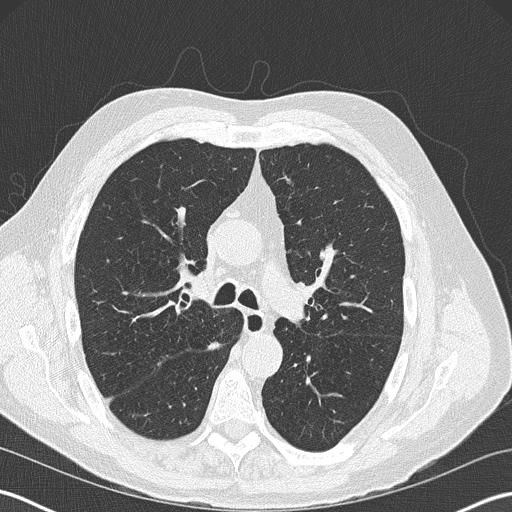
Low-dose screening chest CT, one axial slice. Position 123 of 199 along the scan axis. Reconstruction kernel B50f. Lung window (W 1500 / L -600 HU). 512 × 512 image matrix.
Annotated regions visible in this slice (outlined manually by an expert reader):
- lesion 1 (tumor, upper lobe of right lung): box from (x=153, y=353) to (x=171, y=370) px